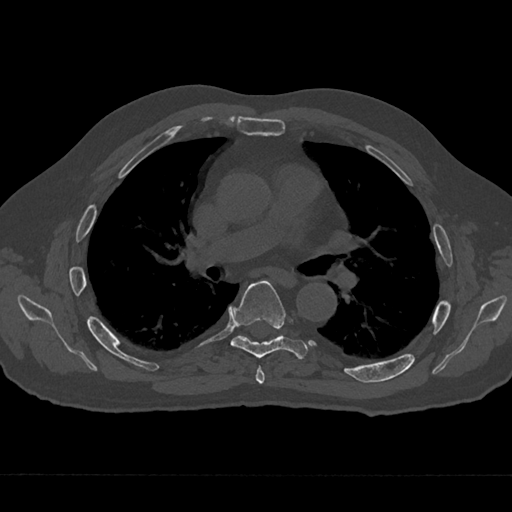
CT including the spine, one axial slice. Slice 422 of 797 in the series (ordered by position). Reconstruction kernel Br40s/3. 120 kVp. Bone window (W 1800 / L 400 HU). 512 × 512 image matrix. Male patient, age 75 years. Case-level facts recorded for this patient, not image findings: primary cancer: renal; vertebrae with lytic lesions (as recorded): T4.
Annotated regions visible in this slice (semi-automatically segmented with operator editing):
- T5 vertebra: box from (x=255, y=366) to (x=265, y=384) px
- T6 vertebra: (x=230, y=280)–(x=308, y=360)